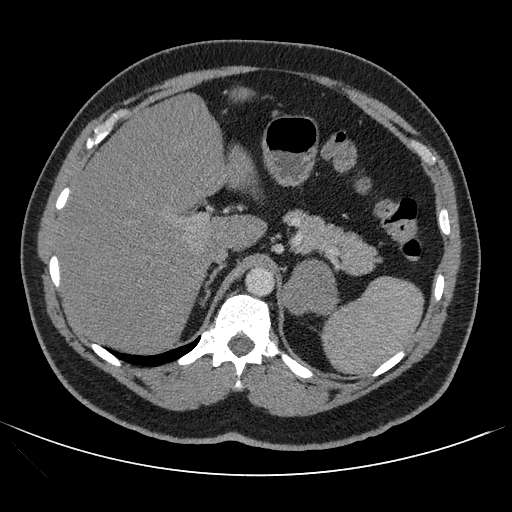
Contrast-enhanced abdominal CT, one axial slice. Slice 76 of 121 in the series (ordered by position). Intravenous contrast given. Soft-tissue window (W 400 / L 40 HU). 2.5 mm slice thickness. 512 × 512 image matrix, field of view 399 × 399 mm. Patient: male, 53 years. Case-level facts recorded for this patient, not image findings: diagnosis: adrenocortical carcinoma; tumour side: left adrenal; tumour size at pathology: 7.9 cm; Ki-67 index: 20 %; stage (as recorded): 2.
Structures marked on this image (semi-automatic segmentation, software-assisted and operator-edited):
- mass: bounding box <282,261,336,314> (left, top, right, bottom; pixels)